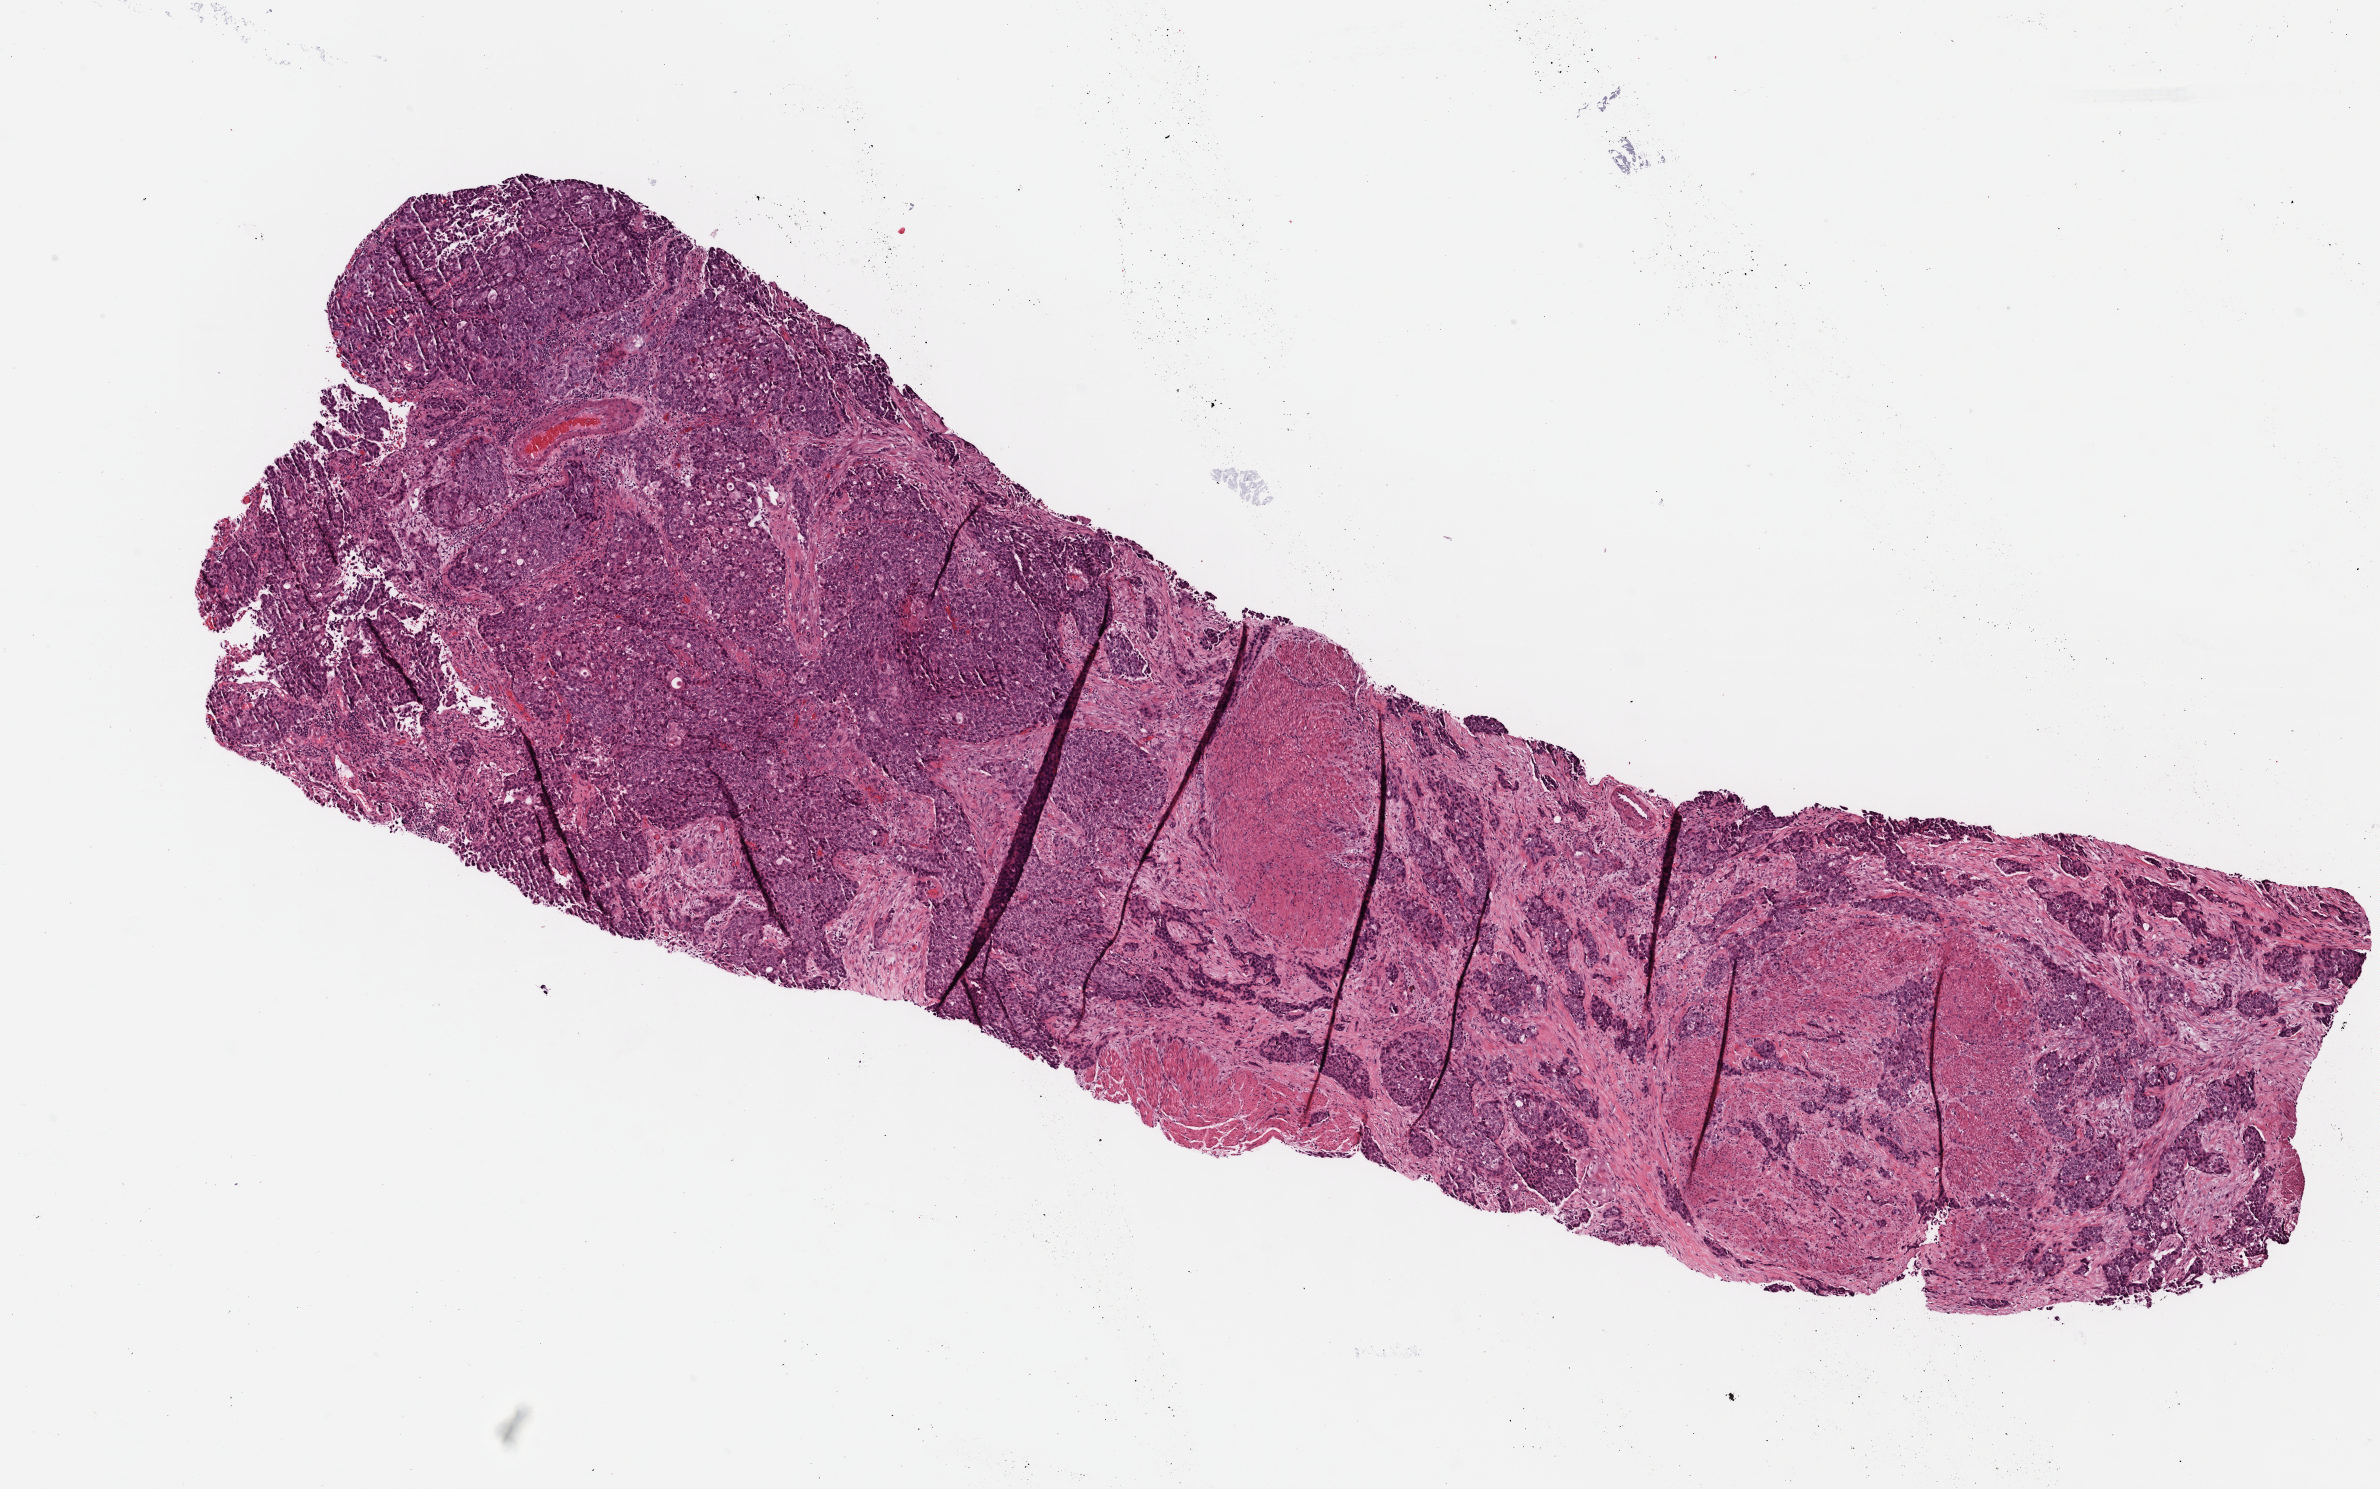
H&E-stained whole-slide image — a low-resolution overview of the entire scanned area, about 9.4 x 5.9 mm (acquisition: 40x scan), formalin-fixed paraffin-embedded (FFPE) diagnostic section, bladder, primary tumour sample. Male, age 65 years at initial diagnosis. Histologic grade: high grade.
Pathologic diagnosis: Transitional cell carcinoma. AJCC pathologic stage: IV. Lymph nodes positive (case pathology): 2 of 11 examined.